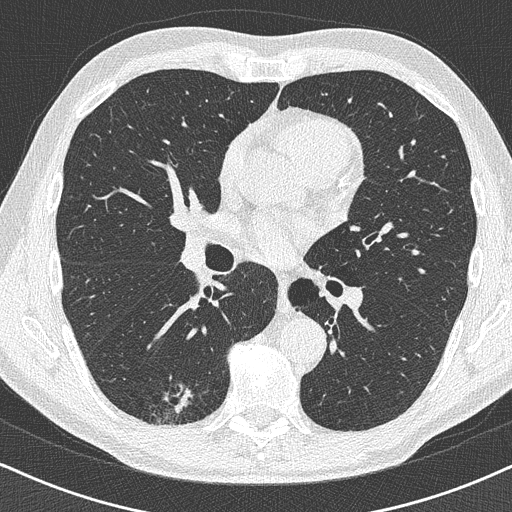
Low-dose screening chest CT, one axial slice. Position 233 of 438 along the scan axis. 120 kVp. Lung window (W 1500 / L -600 HU). 512 × 512 image matrix.
Outlined on this slice (outlined manually by an expert reader):
- lesion 1 (tumor, lower lobe of right lung): bounding box (x1, y1, x2, y2) in pixels: (176, 390, 191, 415)